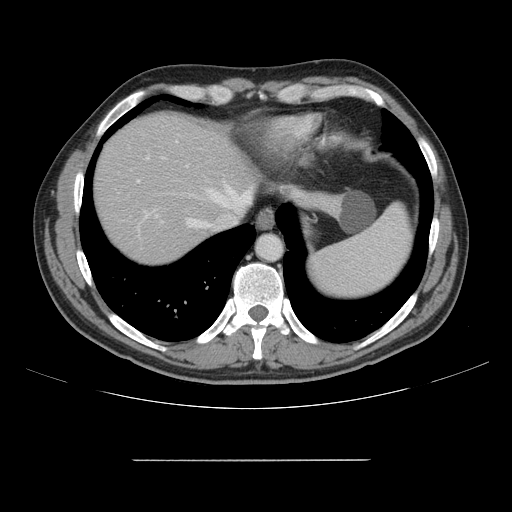
Contrast-enhanced abdominal CT, one axial slice; slice 133 of 164 in the series (ordered by position); intravenous contrast given; soft-tissue window (W 400 / L 40 HU); 512 × 512 image matrix, field of view 404 × 404 mm. Male patient, age 54 years. From the clinical record (not read from this slice): diagnosis: colorectal cancer liver metastases, imaged before liver resection; multiple liver metastases: yes; largest metastasis: 1 cm.
Outlined on this slice (outlined manually by an expert reader):
- hepatic veins: bounding box (x1, y1, x2, y2) in pixels: (186, 189, 250, 227)
- liver: (94, 114, 326, 265)
- planned liver remnant (the part of the liver to remain after resection): (94, 114, 248, 265)
- portal vein (with intrahepatic branches): (137, 141, 209, 218)